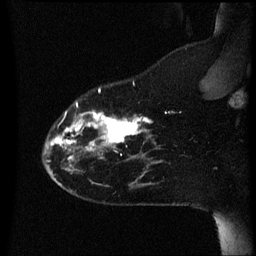
Breast MRI (dynamic contrast-enhanced), one sagittal slice. Slice 13 of 60 in the series (ordered by position). Dynamic contrast-enhanced series, image 2 of 3 at this slice position (ordered by acquisition). 1.5 T. TE 4.2 ms, TR 8.4 ms. 2.2 mm slice thickness. 256 × 256 image matrix, field of view 200 × 200 mm. Female patient, age 35 years. Case-level facts recorded for this patient, not image findings: setting: breast cancer imaged before/during neoadjuvant chemotherapy; receptor status: HER2-positive.
Structures marked on this image (semi-automatic segmentation, software-assisted and operator-edited):
- analysis volume of interest (the breast-tissue region the enhancement analysis was run in; not a lesion): bounding box (x1, y1, x2, y2) in pixels: (44, 80, 168, 173)
- tumour enhancement mask (voxels above the 70 % enhancement threshold inside the analysis volume of interest): (47, 90, 153, 161)